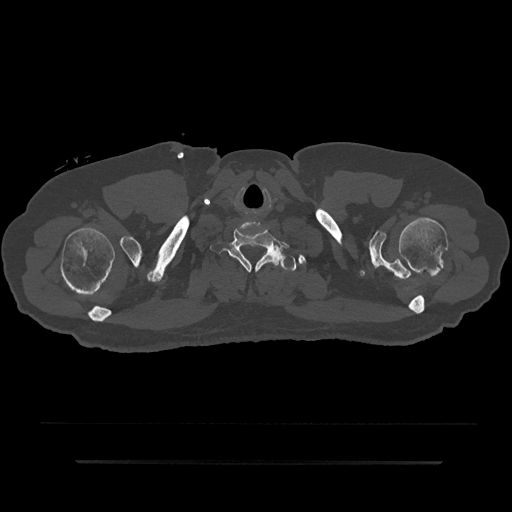
CT including the spine, one axial slice. Position 767 of 797 along the scan axis. 120 kVp. Bone window (W 1800 / L 400 HU). 0.5 mm slice thickness. 512 × 512 image matrix, field of view 464 × 464 mm. Male patient, age 59 years. From the clinical record (not read from this slice): primary cancer: bile ducts.
Structures marked on this image (semi-automatic segmentation, software-assisted and operator-edited):
- T1 vertebra: bounding box (x1, y1, x2, y2) in pixels: (270, 249, 297, 271)